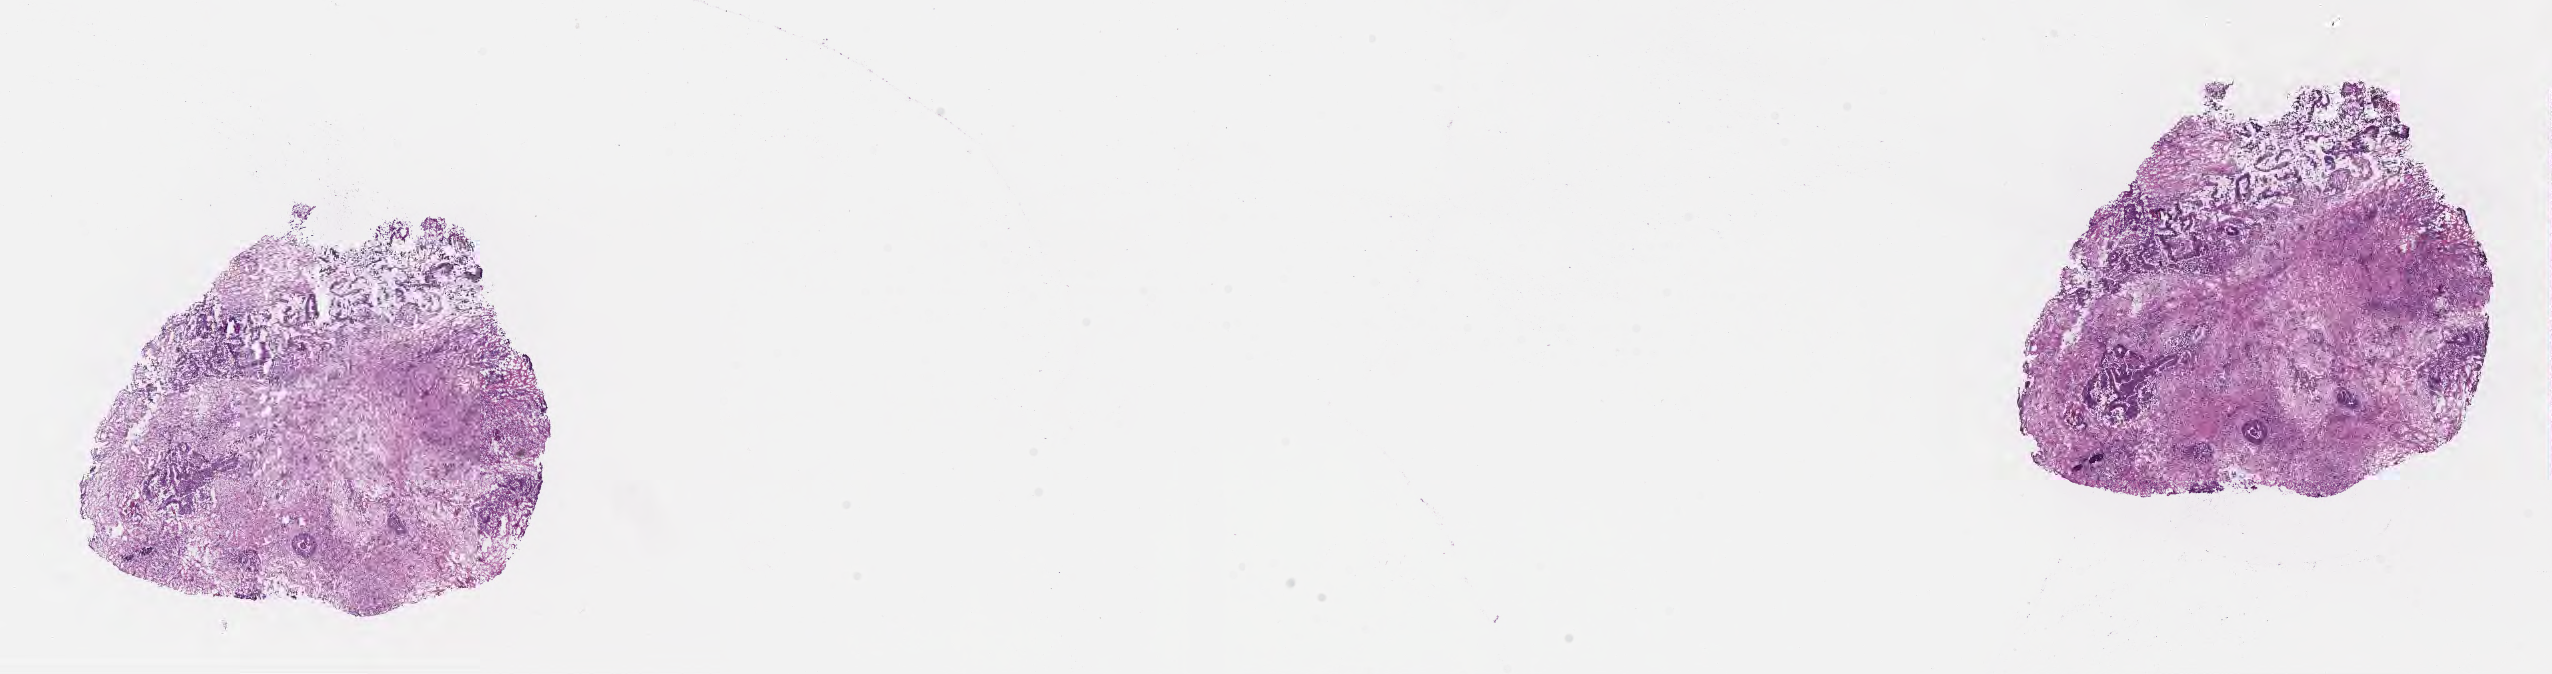
Haematoxylin and eosin whole-slide image, low-resolution overview of the scanned area, about 20.6 x 5.4 mm, cryosection, specimen: primary tumor, anatomic site: sigmoid colon. Male patient; age at initial diagnosis 82 years. Tumor grade: G2 (moderately differentiated). Pathologist review of this section (percent, as recorded): tumor cells 70%, tumor nuclei 50%, stromal cells 0%, necrosis 0%, normal cells 30%. Infiltration values recorded for this section: lymphocyte infiltration 0%, monocyte infiltration 0%, neutrophil infiltration 0%.
Section: bottom of the tissue portion. AJCC pathologic stage: Stage IIA. Diagnosis: Adenocarcinoma, NOS.